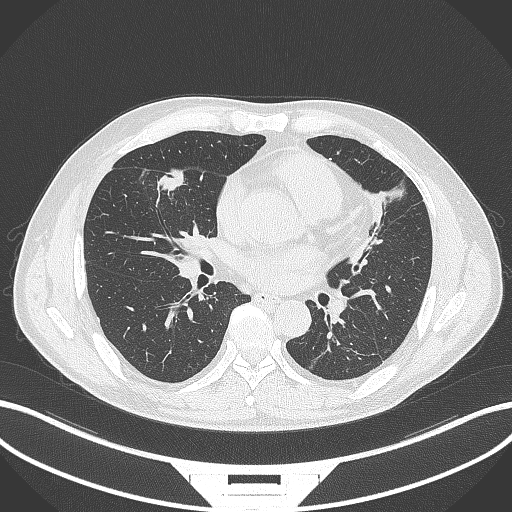
Chest CT, one axial slice. Slice 149 of 399 in the series (ordered by position). Reconstruction kernel B70f. 120 kVp. Lung window (W 1500 / L -600 HU). 1 mm slice thickness. 512 × 512 image matrix, field of view 400 × 400 mm. Patient: male, 59 years. Case-level facts recorded for this patient, not image findings: clinical TNM (as recorded): T2a N1 M0.
Outlined on this slice (rectangle marked by the reading radiologist):
- lung tumour (recorded histology: adenocarcinoma): bounding box <158,165,188,192> (left, top, right, bottom; pixels)